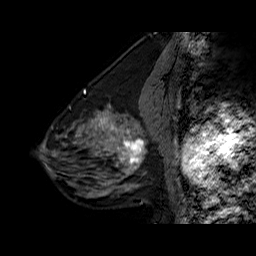
Breast MRI (dynamic contrast-enhanced), one sagittal slice; position 24 of 60 along the scan axis; dynamic contrast-enhanced series, time point 2 of 6 at this slice position (early post-contrast); 1.5 T; TE 6.3 ms, TR 32.5 ms; 256 × 256 image matrix, field of view 200 × 200 mm. Female patient. Case-level facts recorded for this patient, not image findings: setting: breast cancer imaged before/during neoadjuvant chemotherapy; receptor status: triple-negative.
Outlined on this slice (semi-automatic segmentation, software-assisted and operator-edited):
- analysis volume of interest (the breast-tissue region the enhancement analysis was run in; not a lesion): box from (x=108, y=126) to (x=154, y=177) px
- tumour enhancement mask (voxels above the 100 % enhancement threshold inside the analysis volume of interest): (x=108, y=126)–(x=146, y=173)